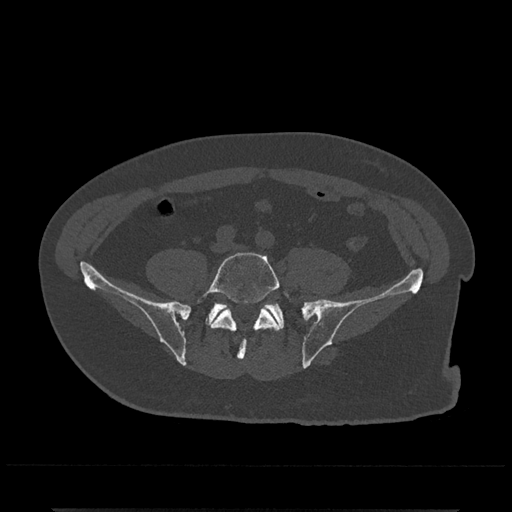
CT including the spine, one axial slice. Position 74 of 797 along the scan axis. Bone window (W 1800 / L 400 HU). 0.5 mm slice thickness. 512 × 512 image matrix, field of view 393 × 393 mm. Patient: male, 67 years. Case-level facts recorded for this patient, not image findings: primary cancer: prostate.
Outlined on this slice (semi-automatically segmented with operator editing):
- L5 vertebra: bounding box <197,252,290,361> (left, top, right, bottom; pixels)